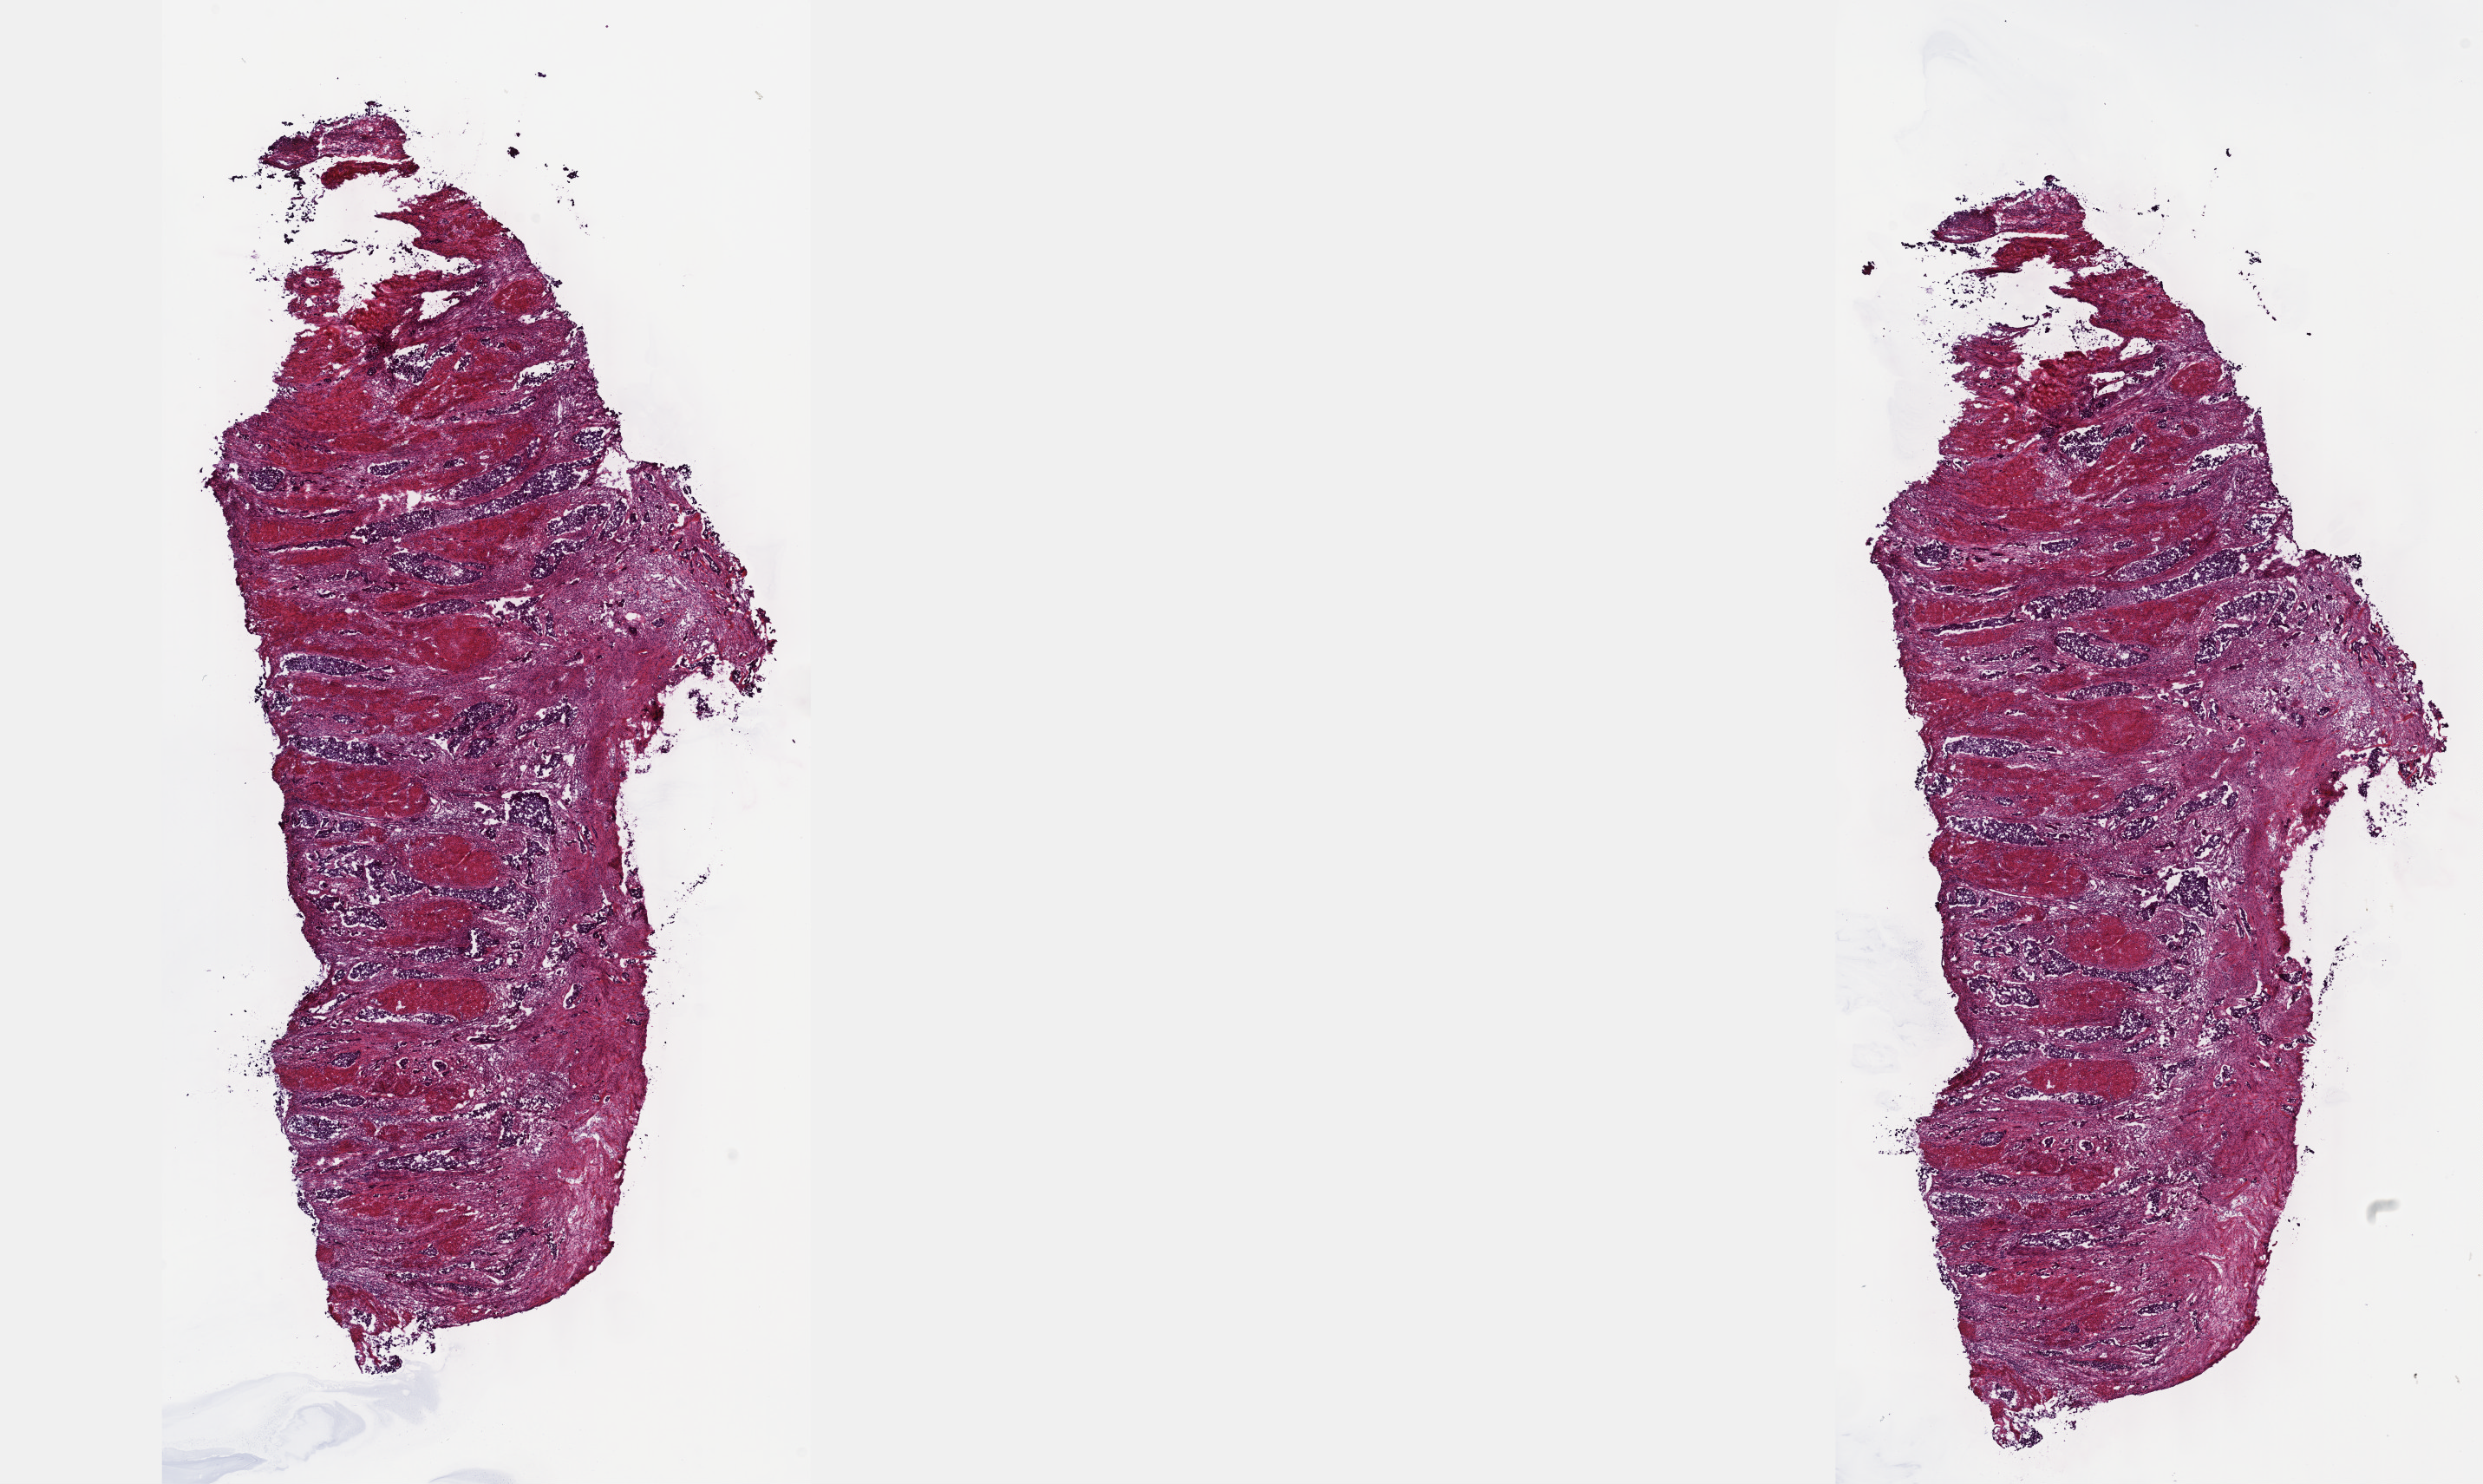
Hematoxylin and eosin (H&E) stained whole-slide image, low-resolution overview of the scanned area, about 23.1 x 13.8 mm (from a 40x scan). Frozen section from the top of the tissue portion. Sample: primary tumour, bladder. Patient: male, age at initial diagnosis 77 years. Histologic grade: high grade. Pathologist review of this section (percent, as recorded): tumour cells 100%, tumour nuclei 60%, normal cells 0%, stromal cells 0%, necrosis 0%. Infiltration values recorded for this section: lymphocyte infiltration 2%, monocyte infiltration 0%, neutrophil infiltration 0%.
AJCC pathologic stage: III. Lymph nodes positive (case pathology): 0 of 18 examined. Pathologic diagnosis: Transitional cell carcinoma (lateral wall of bladder).